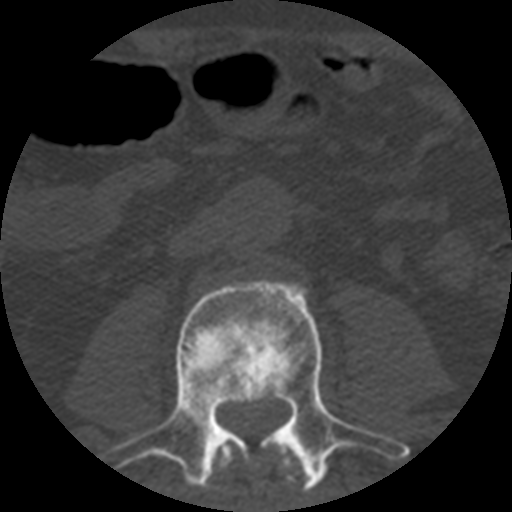
CT including the spine, one axial slice; slice 125 of 508 in the series (ordered by position); reconstruction kernel STANDARD; 120 kVp; bone window (W 1800 / L 400 HU); 1.25 mm slice thickness; 512 × 512 image matrix, field of view 160 × 160 mm. Patient age 57 years. From the clinical record (not read from this slice): primary cancer: prostate.
Annotated regions visible in this slice (semi-automatic segmentation, software-assisted and operator-edited):
- L2 vertebra: bounding box (x1, y1, x2, y2) in pixels: (210, 438, 309, 493)
- L3 vertebra: (96, 280, 410, 490)